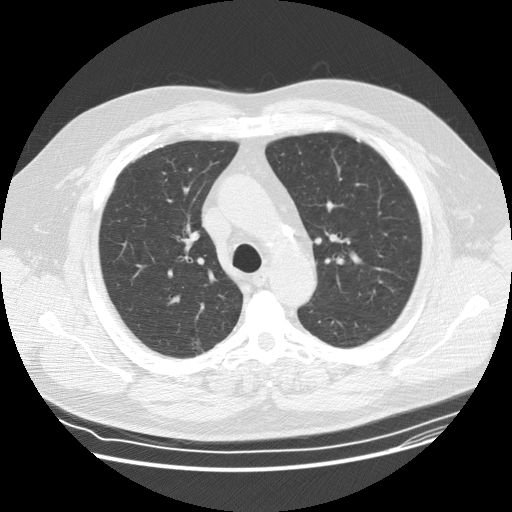
Chest CT (low-dose screening protocol), one axial image; baseline screening round; lung window (W 1500 / L -600 HU); 2.5 mm slice thickness; standard (soft-tissue) reconstruction kernel (STANDARD); 120 kVp; slice 46 of 162 in the series; 512 × 512 image matrix. Male, age 62 years at enrolment. Former smoker at enrolment.
• Expert-annotated lung lesion, box from (x=178, y=332) to (x=218, y=365) px.
• Screening reader's record for this exam (one nodule recorded; not confirmed to be the boxed lesion): non-calcified nodule or mass ≥4 mm, right upper lobe, 8 × 7 mm, smooth margins, ground glass attenuation.
• Official screen result: positive, change unspecified: nodule(s) >= 4 mm or enlarging nodule(s), mass(es), or other non-specific abnormalities suspicious for lung cancer.
• Later outcome: lung cancer diagnosed 795 days after this screen — bronchiolo-alveolar adenocarcinoma, NOS, right upper lobe, well differentiated (G1), stage IA (AJCC 6th edition), 12 mm at pathology.